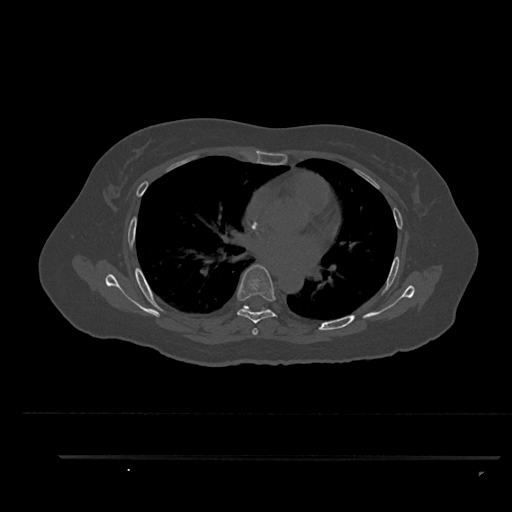
CT including the spine, one axial slice; position 554 of 797 along the scan axis; reconstruction kernel Br40s/3; 120 kVp; bone window (W 1800 / L 400 HU); 512 × 512 image matrix, field of view 408 × 408 mm. Female patient, age 44 years. Case-level facts recorded for this patient, not image findings: primary cancer: renal.
Outlined on this slice (semi-automatic segmentation, software-assisted and operator-edited):
- T6 vertebra: bounding box <237,264,277,335> (left, top, right, bottom; pixels)